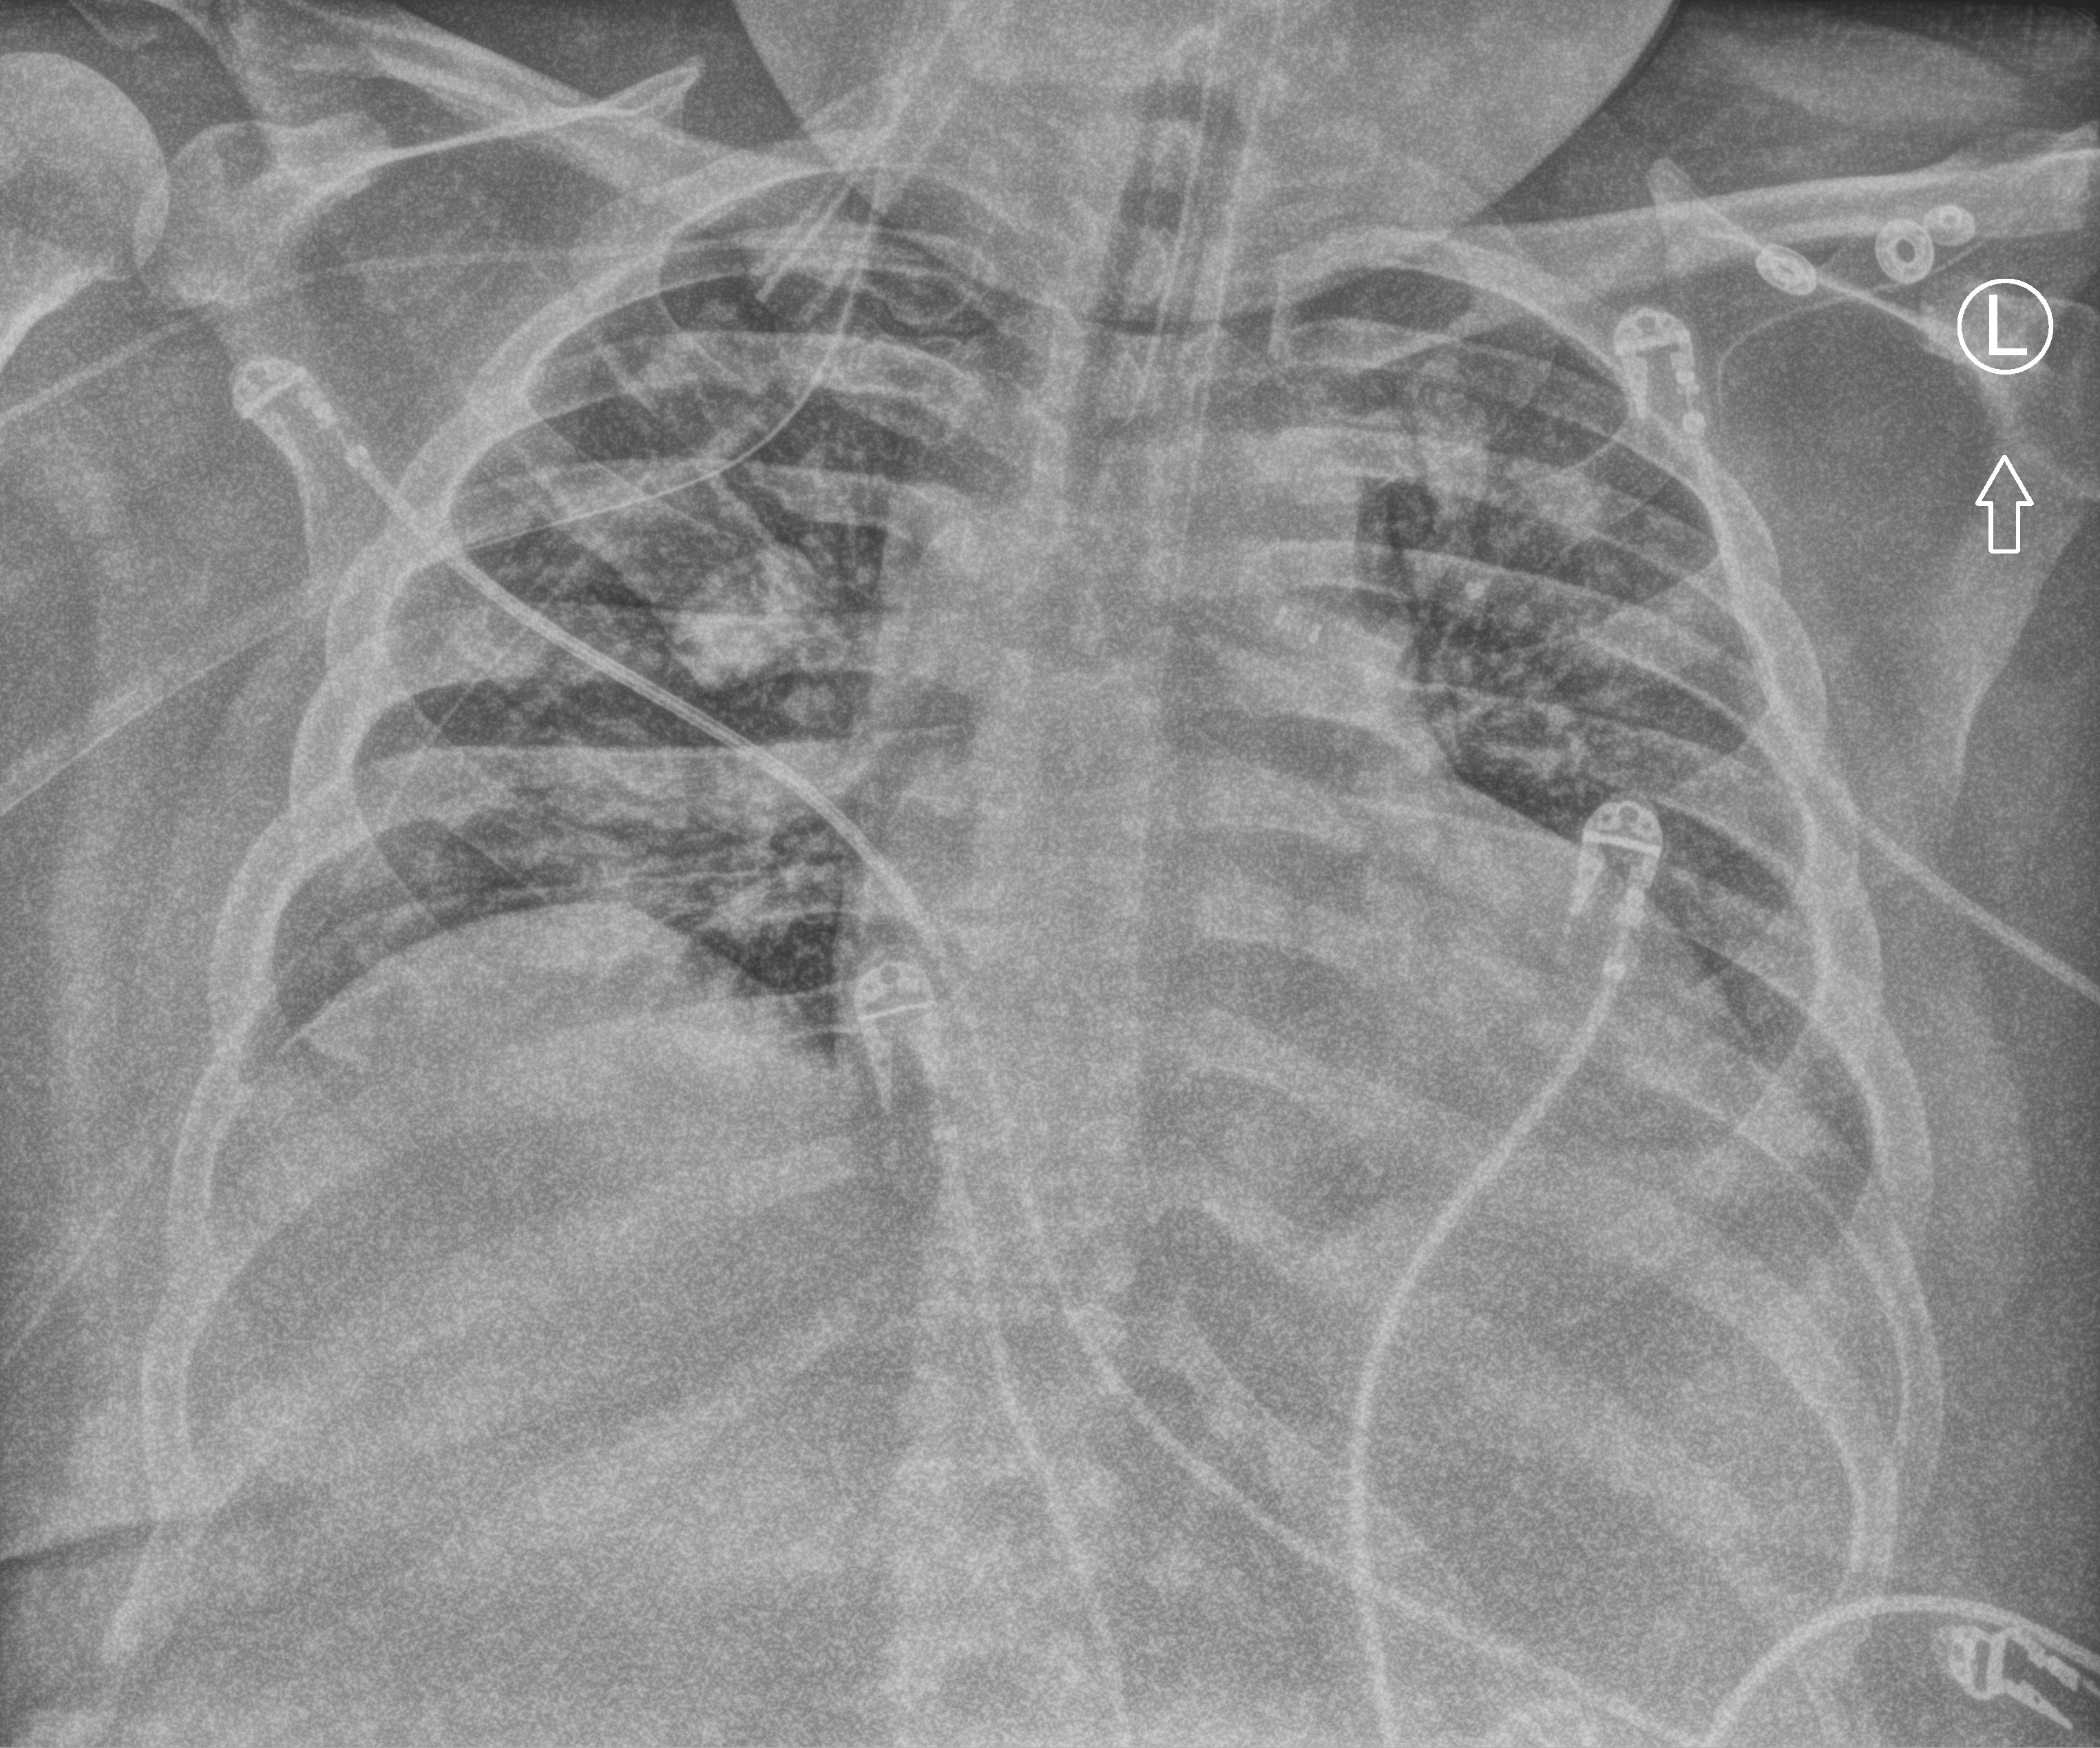
Chest X-ray (portable). Patient hospitalised with COVID-19, aged 18–59 years.
Admission-level facts for this patient (not findings on this image; timing relative to this image not recorded): mechanically ventilated during this hospital stay: yes; admitted to intensive care during this hospital stay: yes.